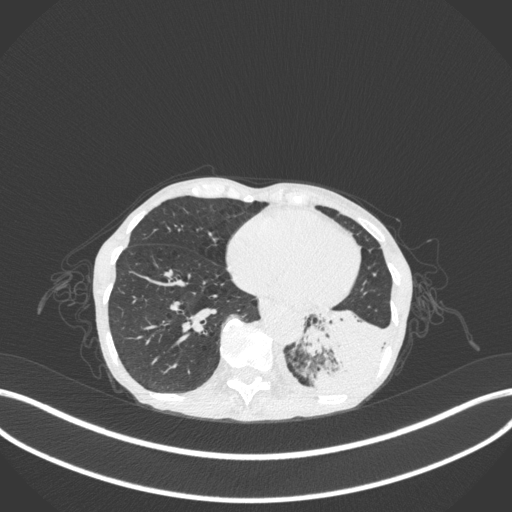
Chest CT, one axial slice; position 71 of 347 along the scan axis; 120 kVp; lung window (W 1500 / L -600 HU); 1 mm slice thickness; 512 × 512 image matrix. Patient: female, 70 years. Case-level facts recorded for this patient, not image findings: clinical TNM (as recorded): T3 N0 M0; histopathological grade: G3.
Outlined on this slice (bounding box drawn by a radiologist):
- lung tumour (recorded histology: small cell carcinoma): box from (x=298, y=301) to (x=384, y=397) px